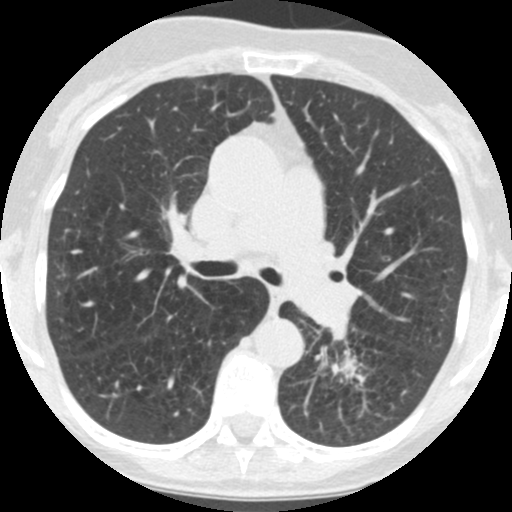
Chest CT (low-dose screening protocol), one axial image; third annual screen; lung window (W 1500 / L -600 HU); 2.5 mm slice thickness; standard (soft-tissue) reconstruction kernel (STANDARD); slice 63 of 171 in the series. Female, age 71 years at enrolment.
Lesion marked by an expert reader, box from (x=307, y=323) to (x=386, y=410) px. The screening reader recorded 2 non-calcified nodules or masses ≥4 mm on this exam (left lower lobe, left lower lobe); which of them this box marks is not recorded.